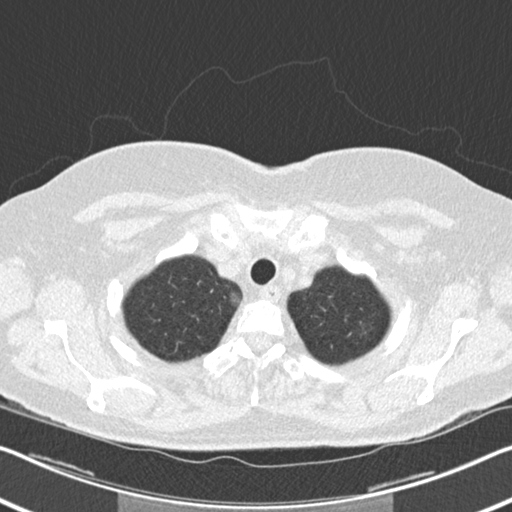
Low-dose screening chest CT, axial slice; second annual screen; lung window (W 1500 / L -600 HU); 2 mm slice thickness; standard (soft-tissue) reconstruction kernel (B30f); slice 29 of 202 in the series; 512 × 512 image matrix, field of view 336 × 336 mm. Female participant, aged 60 years at enrolment. Current smoker at enrolment.
• Expert-annotated lung lesion, bounding box (x1, y1, x2, y2) in pixels: (339, 309, 382, 350).
• The screening reader recorded 6 non-calcified nodules or masses ≥4 mm on this exam (right upper lobe, right middle lobe, right lower lobe, right lower lobe, left lower lobe, lingula); which of them this box marks is not recorded.
• Participant outcome: lung cancer diagnosed 495 days after this screen — non-small cell carcinoma, left upper lobe, poorly differentiated (G3), stage IB (AJCC 6th edition), 7 mm at pathology.